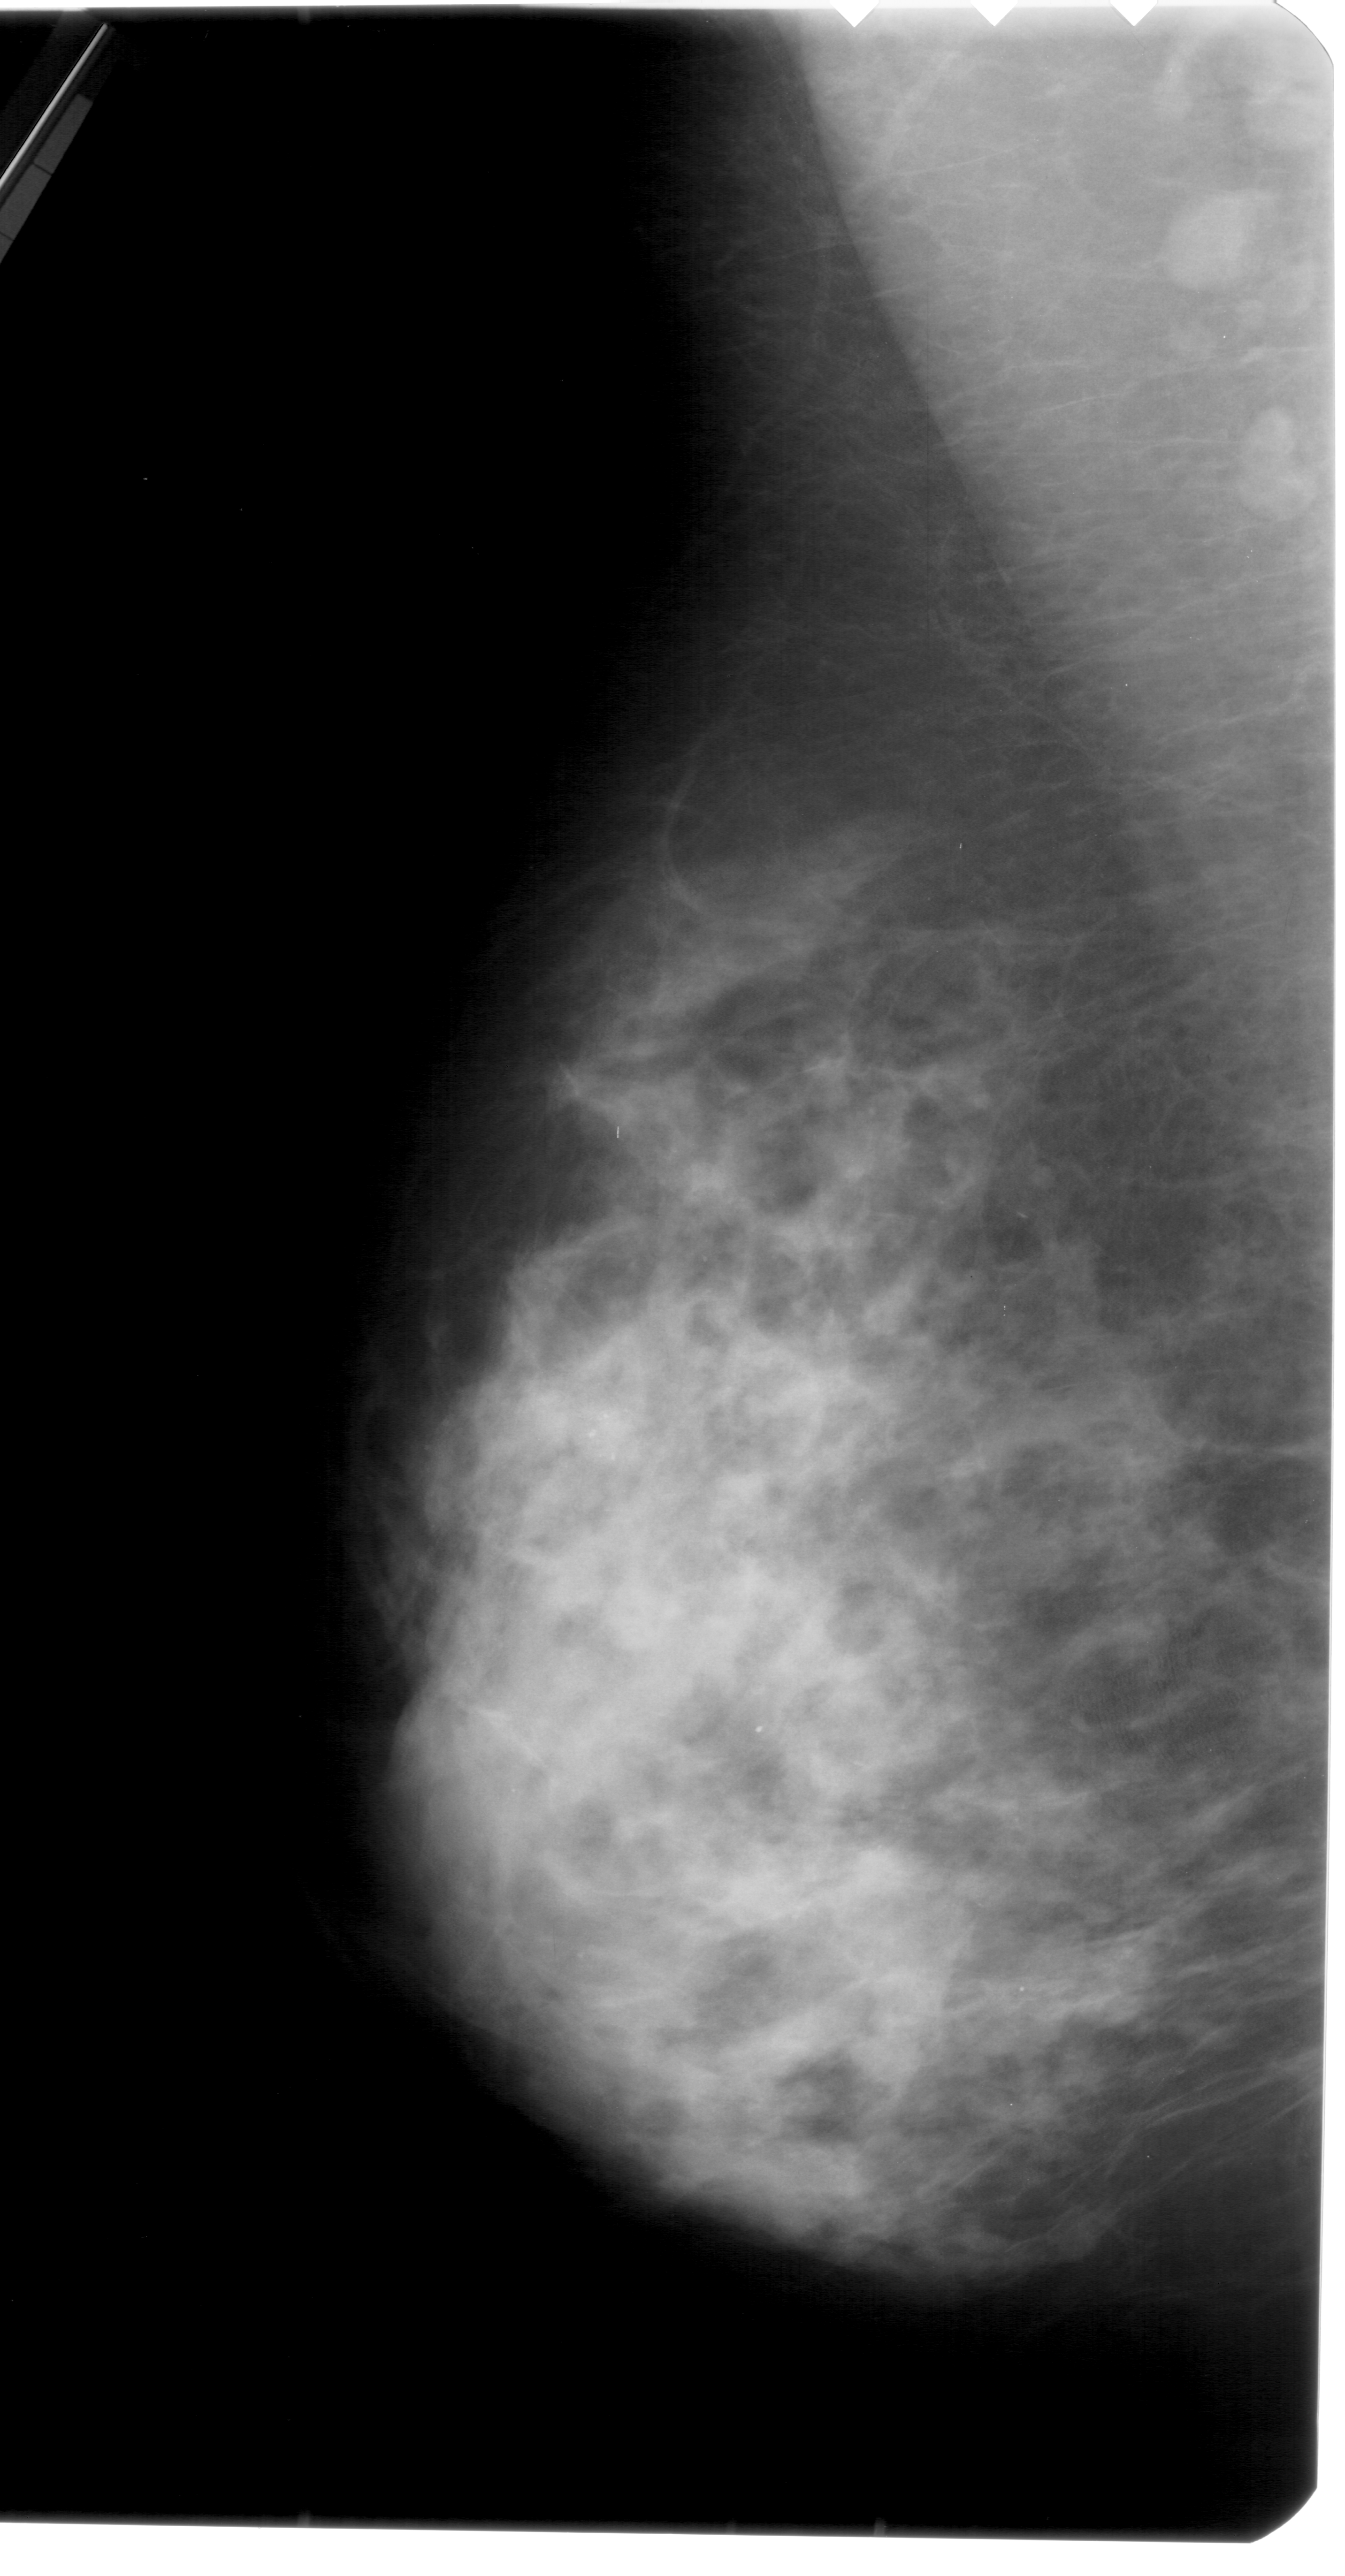
Mammogram (digitized film), left breast, MLO view, BI-RADS breast density category 4 (scale 1–4).
- Finding: calcifications, morphology pleomorphic, distribution clustered; BI-RADS assessment category 4; subtlety rating 4 on a 1 (subtle) to 5 (obvious) scale; pathology (as recorded): malignant.